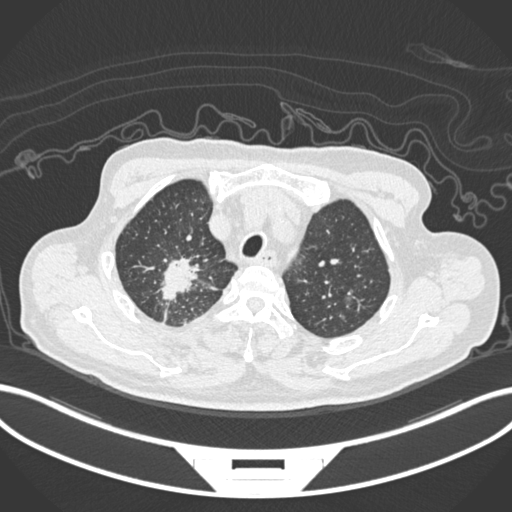
Chest CT, one axial slice; position 176 of 207 along the scan axis; reconstruction kernel B30f; 120 kVp; lung window (W 1500 / L -600 HU); 1 mm slice thickness; 512 × 512 image matrix, field of view 400 × 400 mm. Male patient, age 69 years. Case-level facts recorded for this patient, not image findings: clinical TNM (as recorded): T1c N1 M1.
Structures marked on this image (rectangle marked by the reading radiologist):
- lung tumour (recorded histology: adenocarcinoma): box from (x=149, y=248) to (x=210, y=312) px